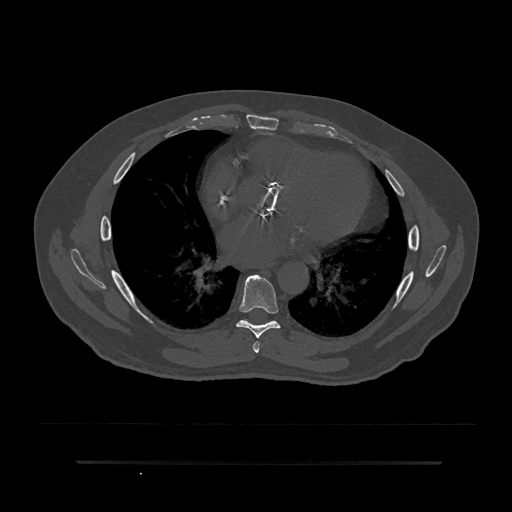
CT including the spine, one axial slice. Slice 474 of 797 in the series (ordered by position). Reconstruction kernel Br40s/3. Bone window (W 1800 / L 400 HU). 0.5 mm slice thickness. 512 × 512 image matrix, field of view 464 × 464 mm. Patient: male, 59 years. Case-level facts recorded for this patient, not image findings: primary cancer: bile ducts.
Structures marked on this image (semi-automatic segmentation, software-assisted and operator-edited):
- T6 vertebra: bounding box (x1, y1, x2, y2) in pixels: (253, 341, 260, 353)
- T7 vertebra: (236, 274, 281, 338)
- T8 vertebra: (242, 319, 246, 321)